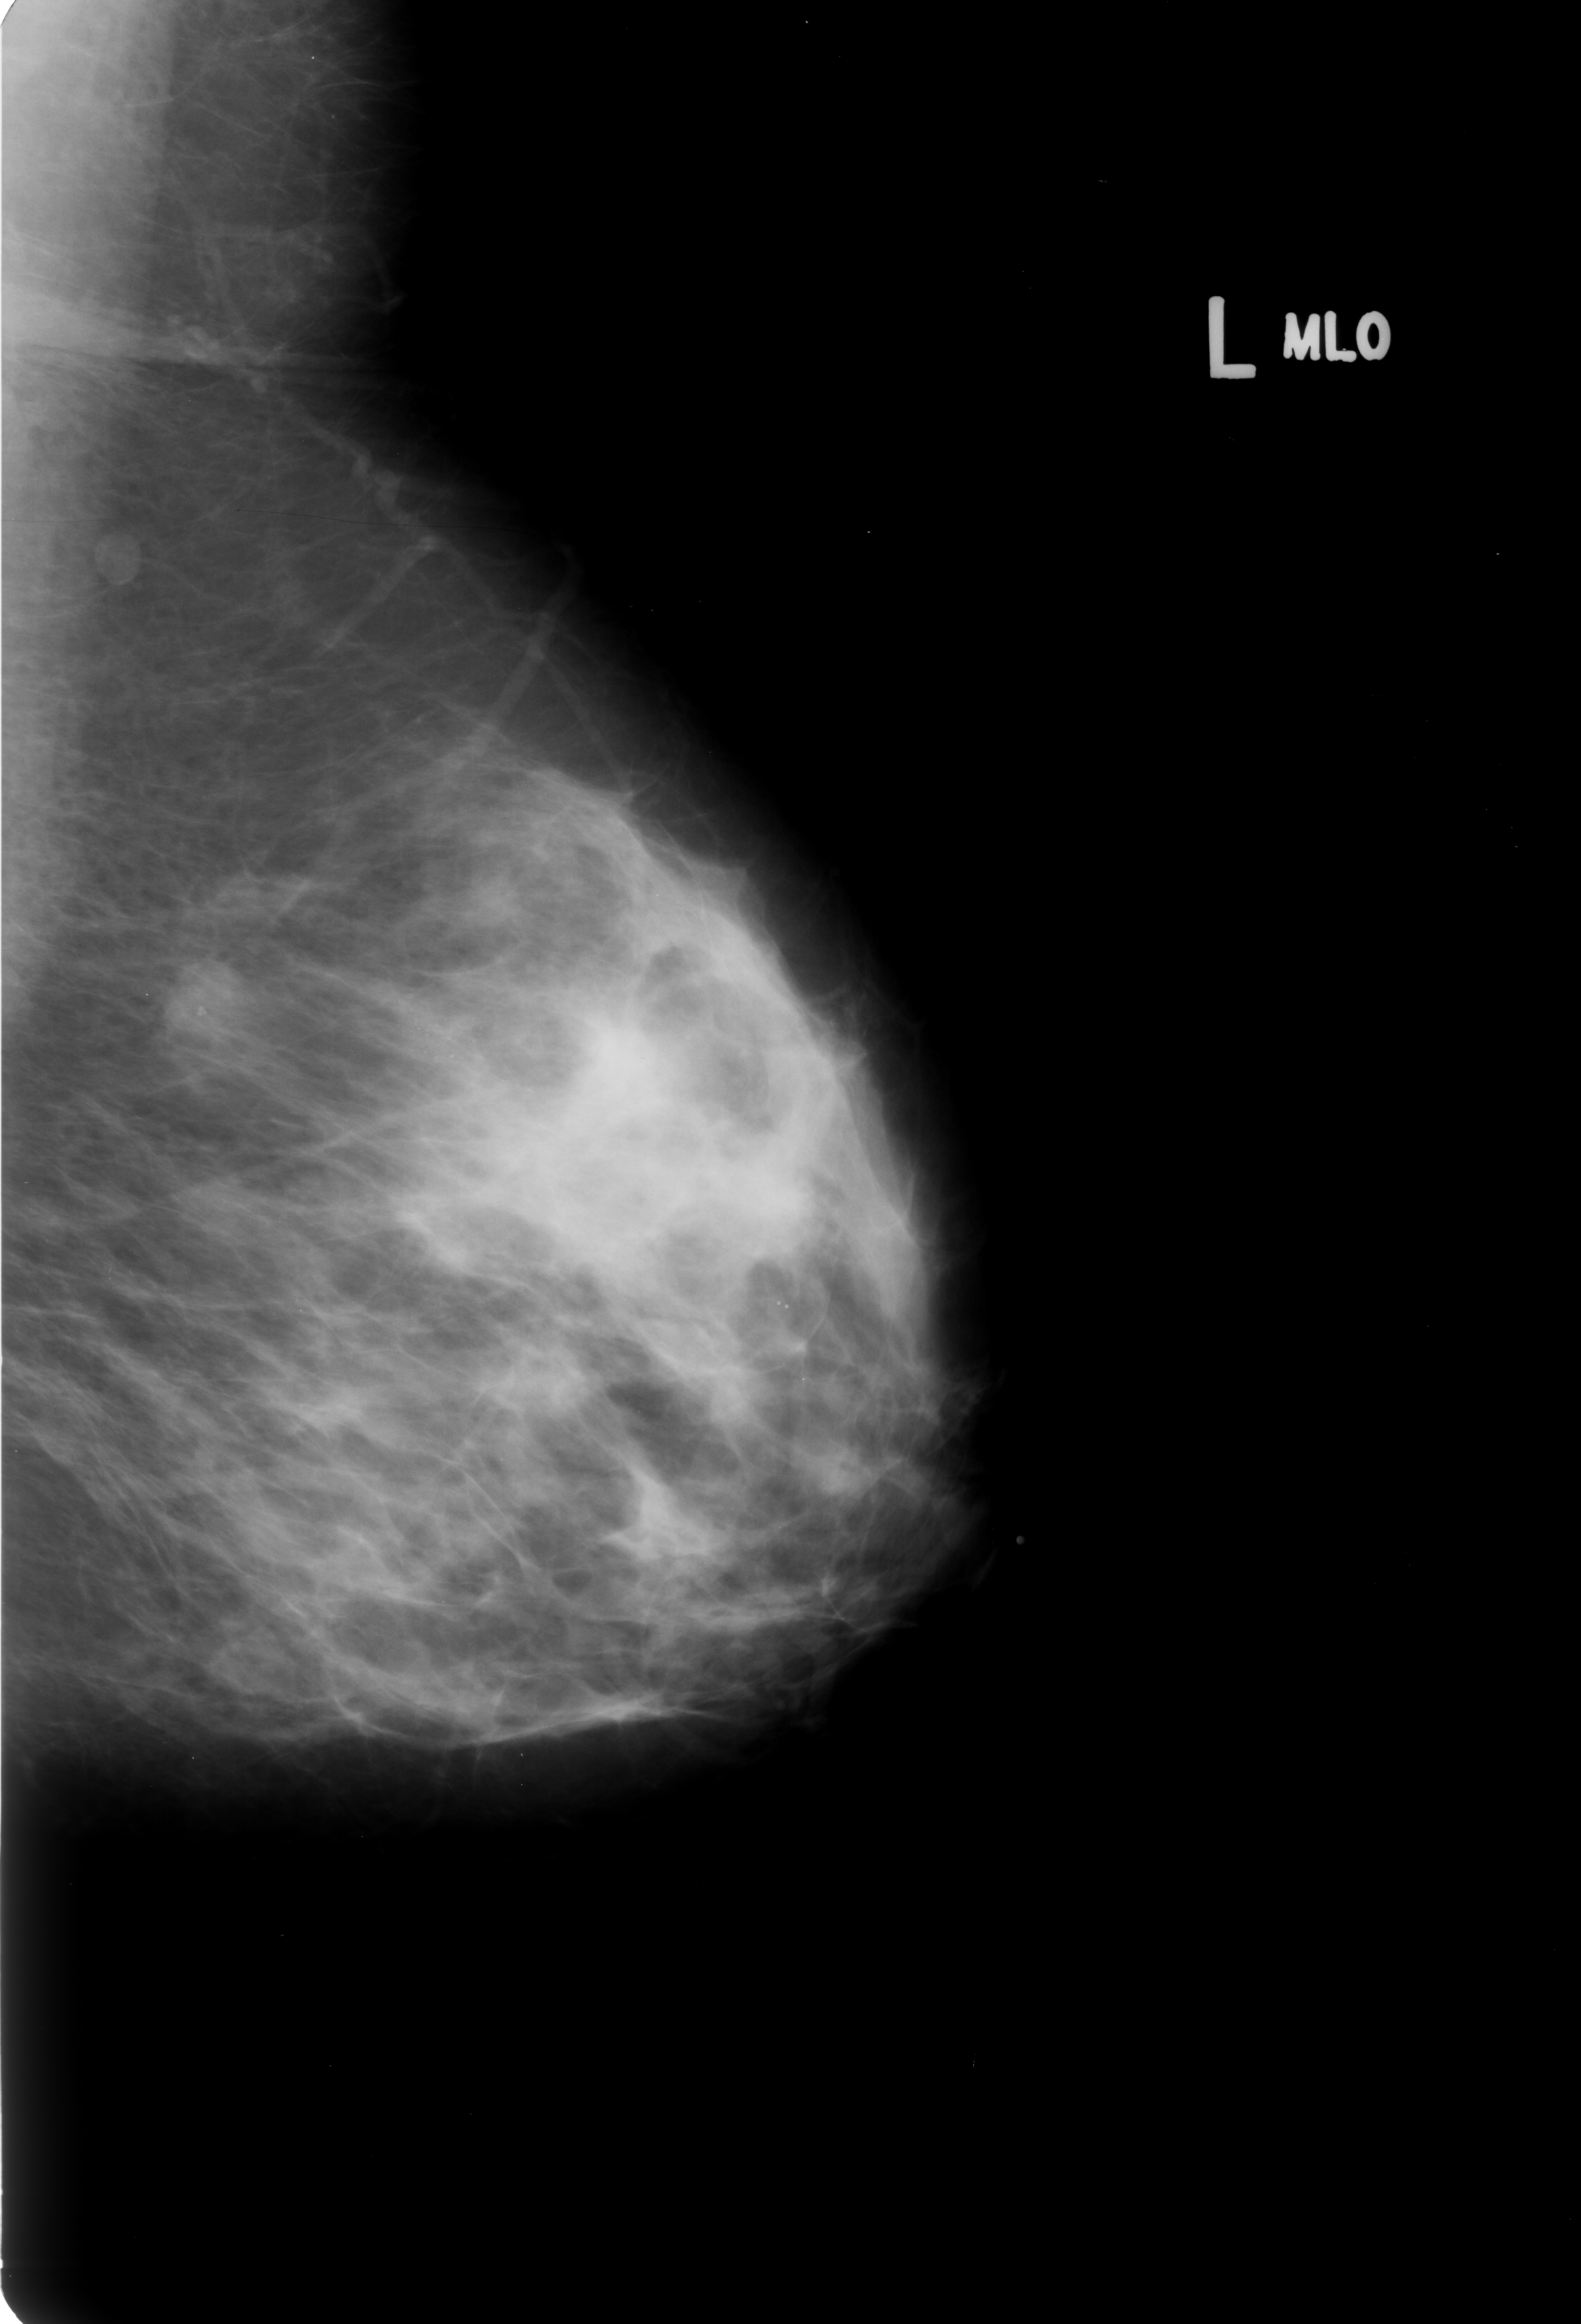
Mammogram (digitized film); left breast; mediolateral oblique (MLO) view; 1581 × 2324 image matrix.
Marked abnormalities (boxes around the expert regions of interest):
- Finding 1 of 2: calcifications, morphology punctate, distribution segmental; BI-RADS assessment category 4; pathology (as recorded): benign: bounding box (x1, y1, x2, y2) in pixels: (354, 992, 513, 1114)
- Finding 2 of 2: calcifications, morphology punctate, distribution segmental; BI-RADS assessment category 4; subtlety rating 3 on a 1 (subtle) to 5 (obvious) scale; pathology result (as recorded, not read from the image): benign: (597, 1163, 671, 1234)